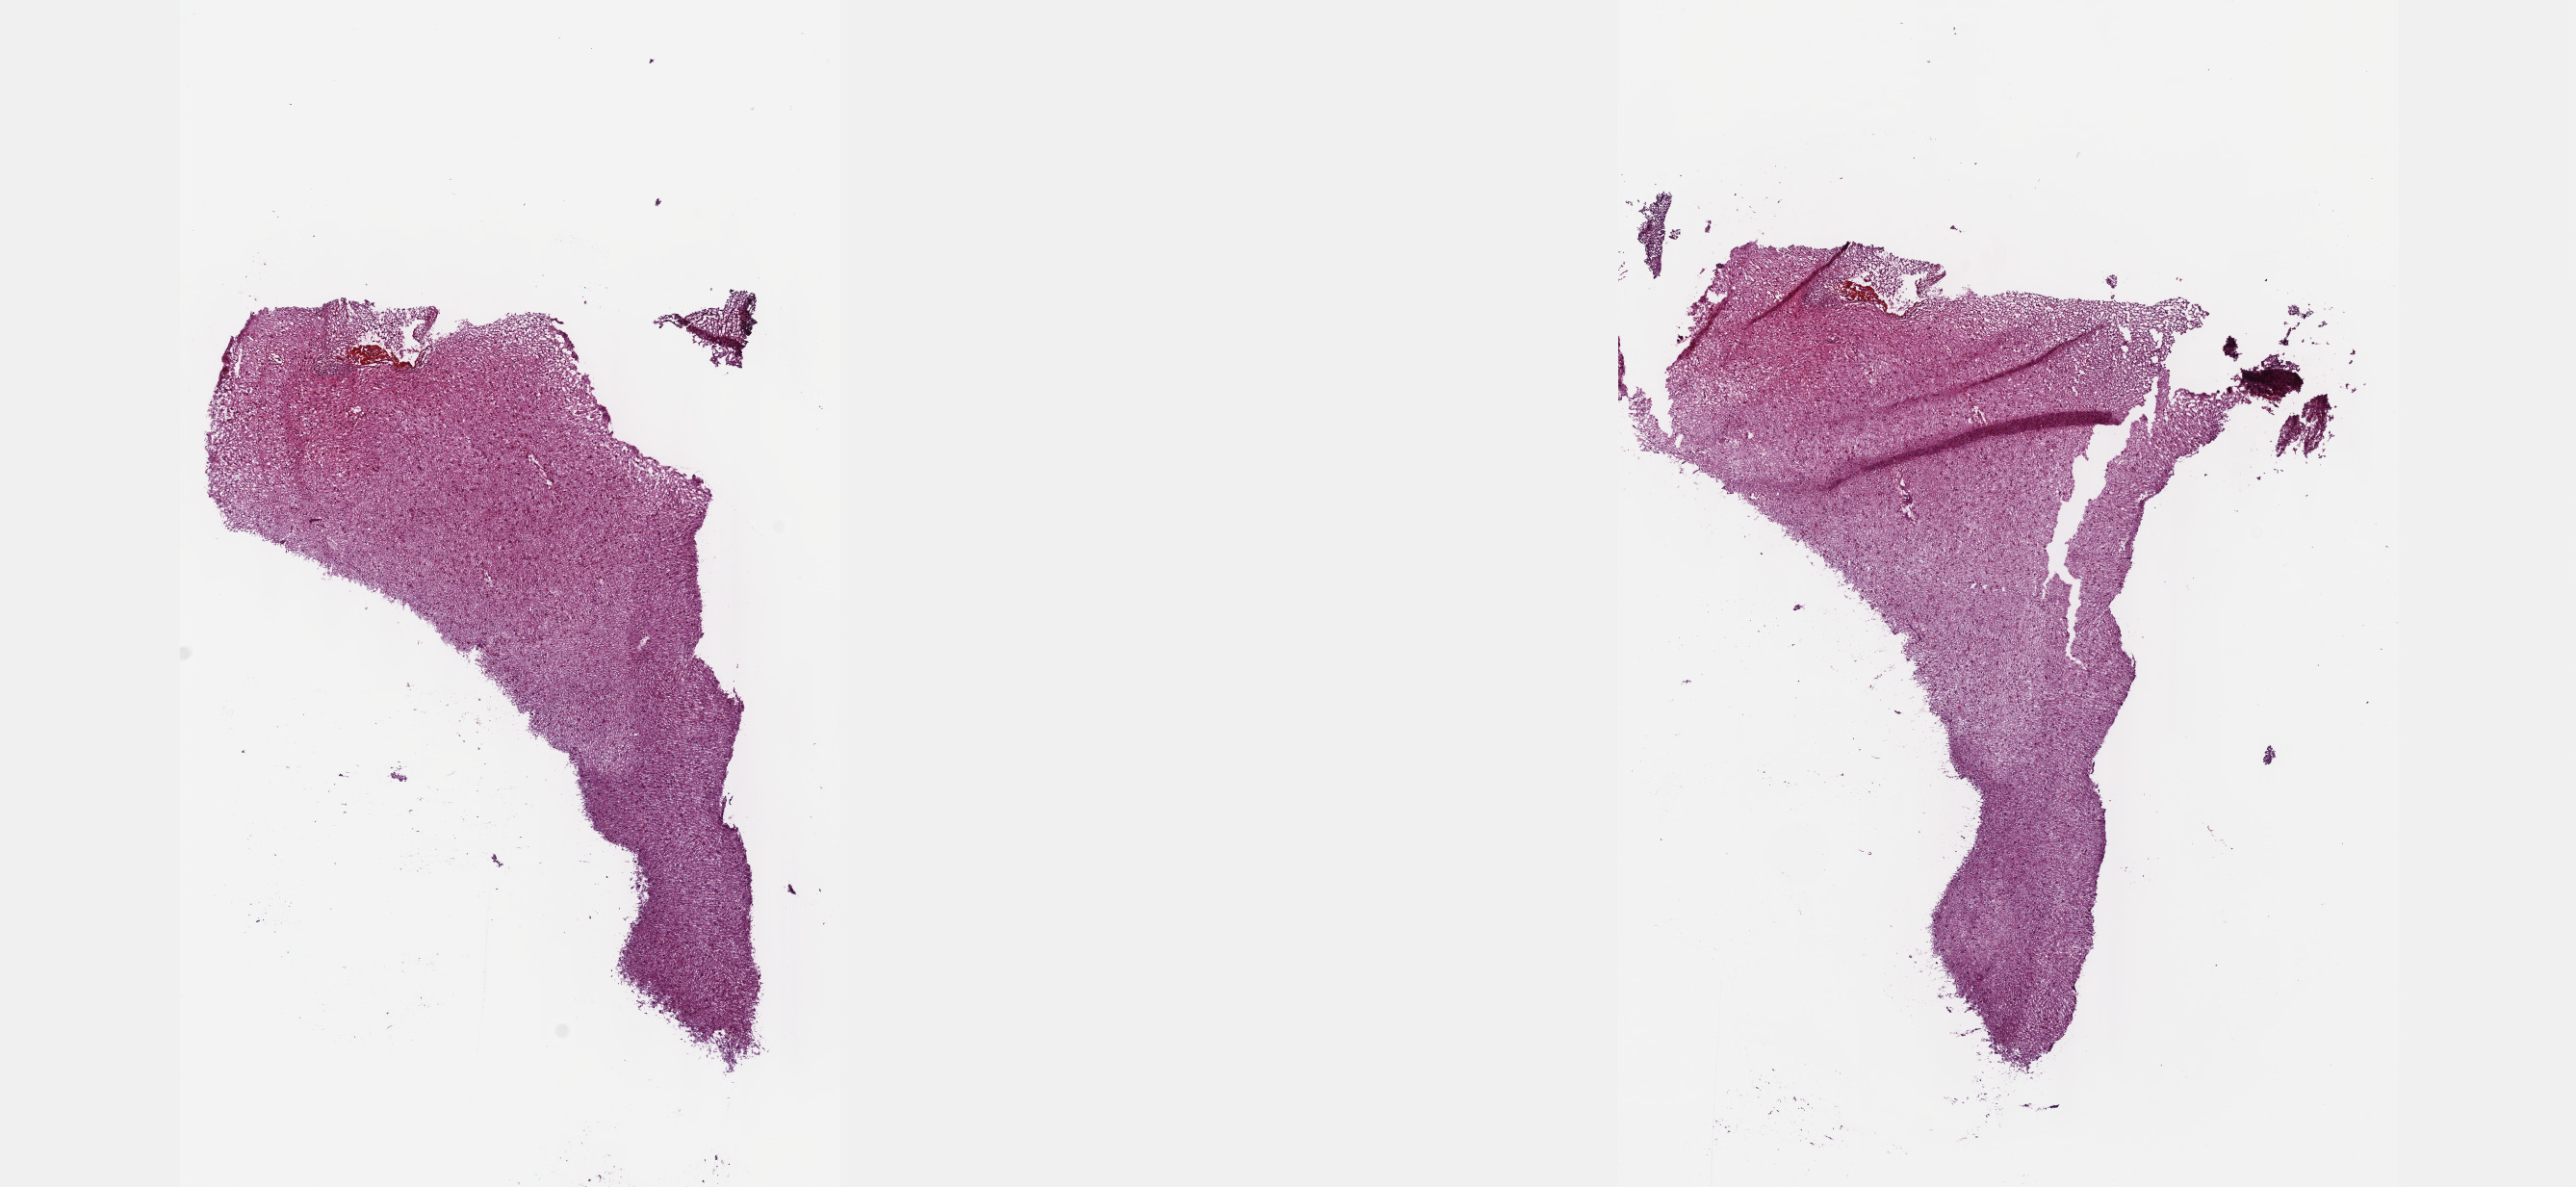
H&E-stained whole-slide image — a low-resolution overview of the entire scanned area, about 21.6 x 10.0 mm. Frozen section from the top of the tissue portion. Sample: primary tumour, brain. Male patient; age at initial diagnosis 52 years. Histologic grade: G3 (poorly differentiated). Slide review estimates, as recorded: tumour cells 50%, tumour nuclei 90%, normal cells 5%, stromal cells 45%, necrosis 0%. Infiltration values recorded for this section: lymphocyte infiltration 0%, monocyte infiltration 0%, neutrophil infiltration 0%.
• laterality: left
• histologic diagnosis: Astrocytoma, anaplastic